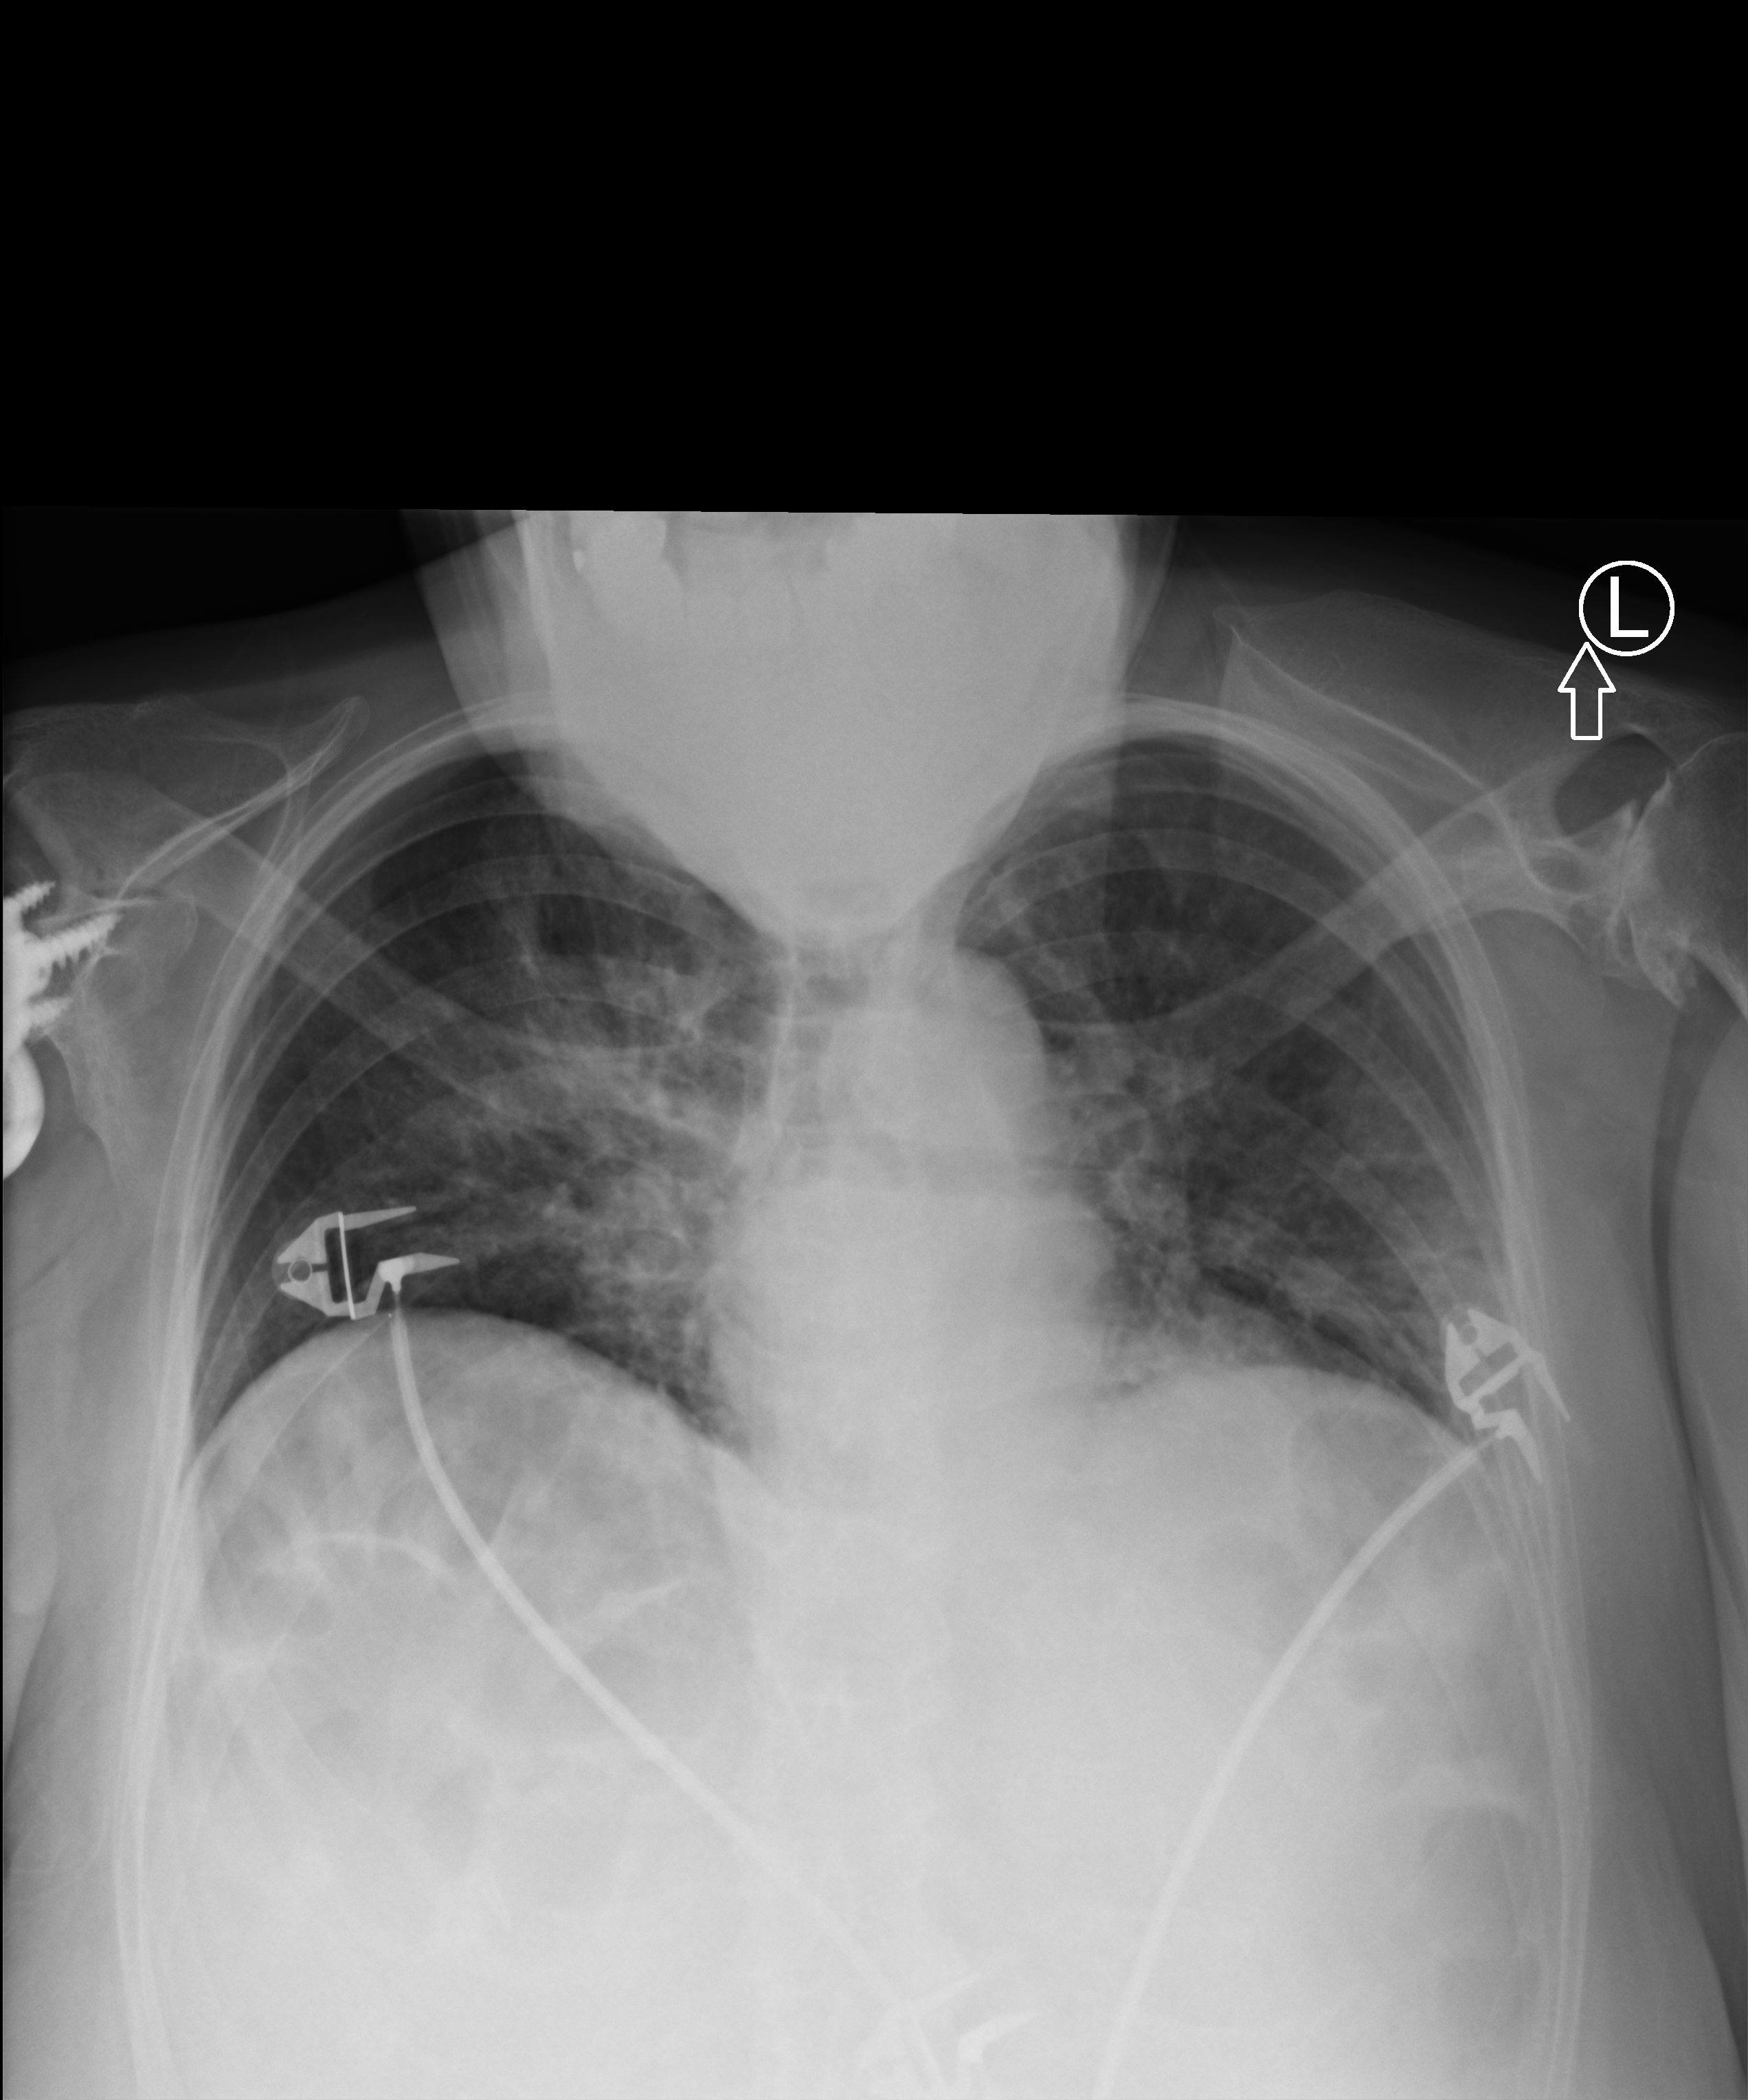
Portable chest radiograph; anteroposterior (AP) projection. Patient hospitalised with COVID-19; female, aged 60–74 years.
From the hospital-stay record, not from the radiograph (when in the stay this image was taken is not recorded): admitted to intensive care during this hospital stay: yes.